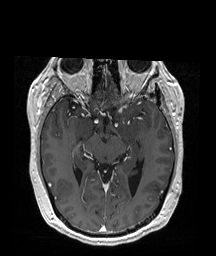
Brain MRI from a brain-tumour surgery series, one axial slice. T1-weighted post-contrast. 216 × 256 image matrix, field of view 211 × 250 mm. Case-level facts recorded for this patient, not image findings: histopathology: Oligodendroglioma; WHO grade: 2; IDH mutation: yes; tumour location: Left Frontal (septal).
Outlined on this slice (outlined manually by an expert reader):
- tumour: bounding box (x1, y1, x2, y2) in pixels: (108, 102, 114, 108)